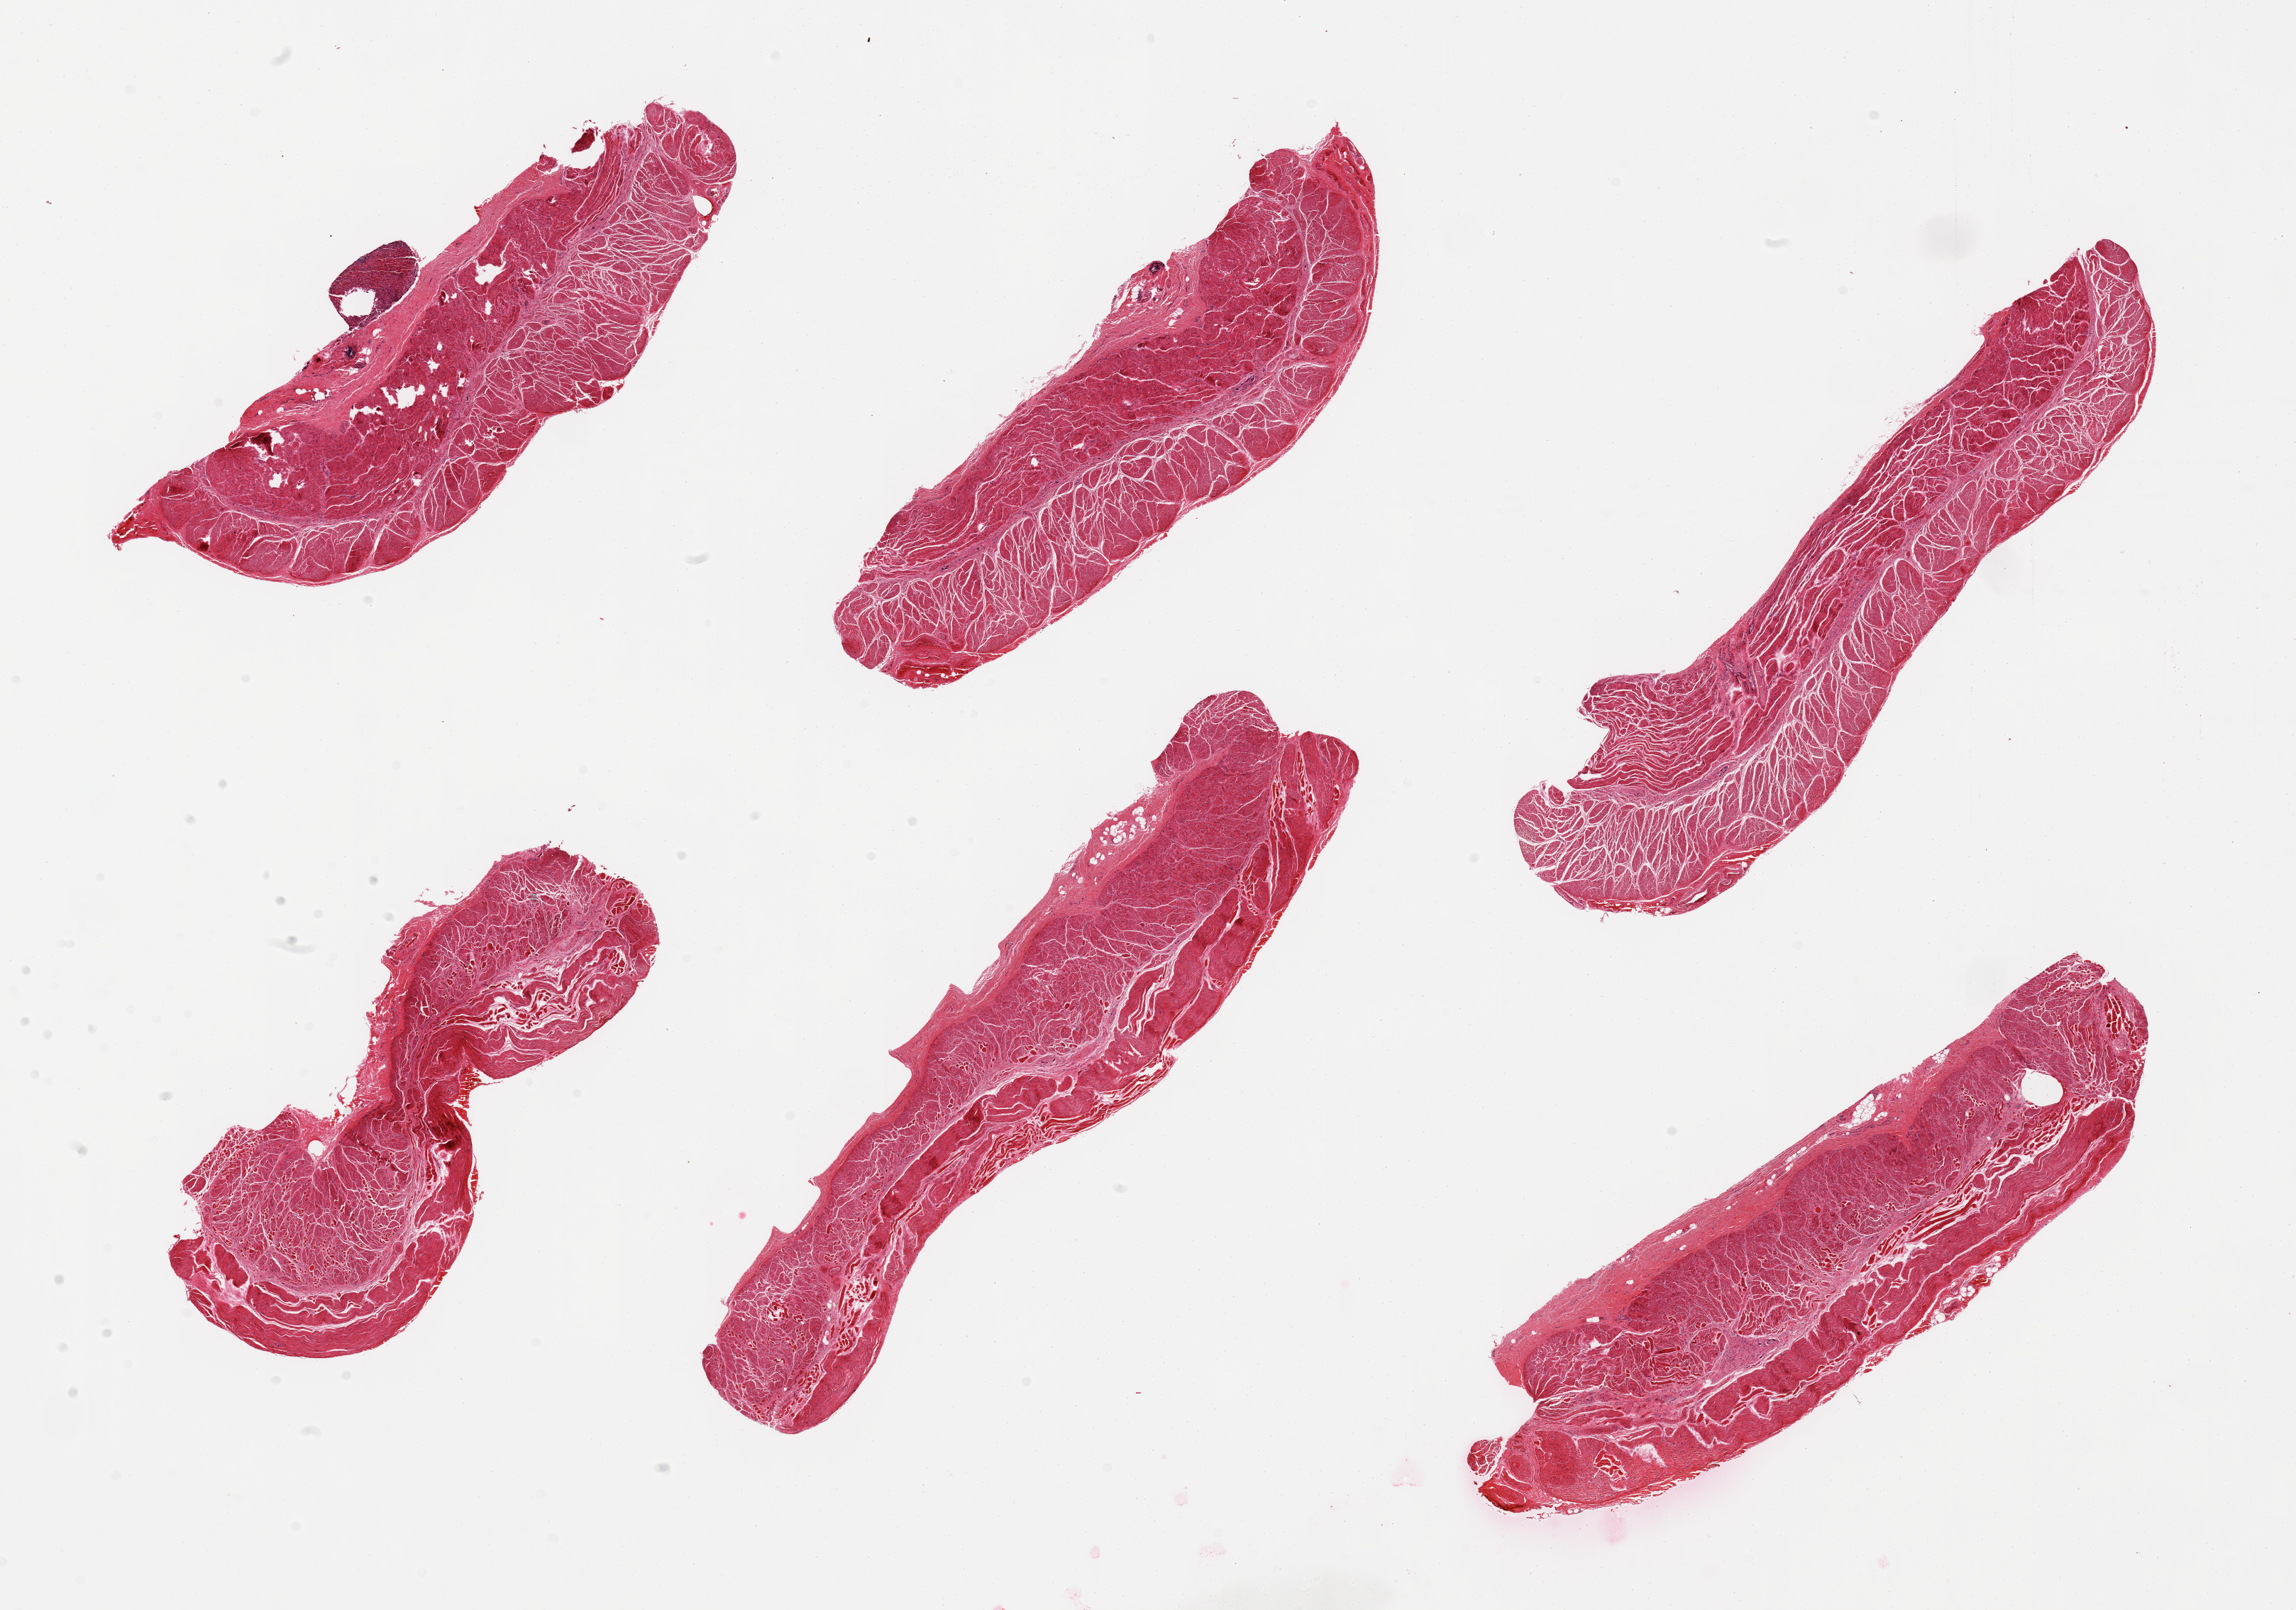
Haematoxylin and eosin whole-slide image — whole scanned area (about 25.6 x 17.9 mm) shown as a low-resolution overview; PAXgene-fixed, paraffin-embedded tissue; target tissue: esophageal muscle; donor tissue sample. Donor: male.
- pathologist's review note for this sample: 6 pieces; 1 mm carry-over from spleen